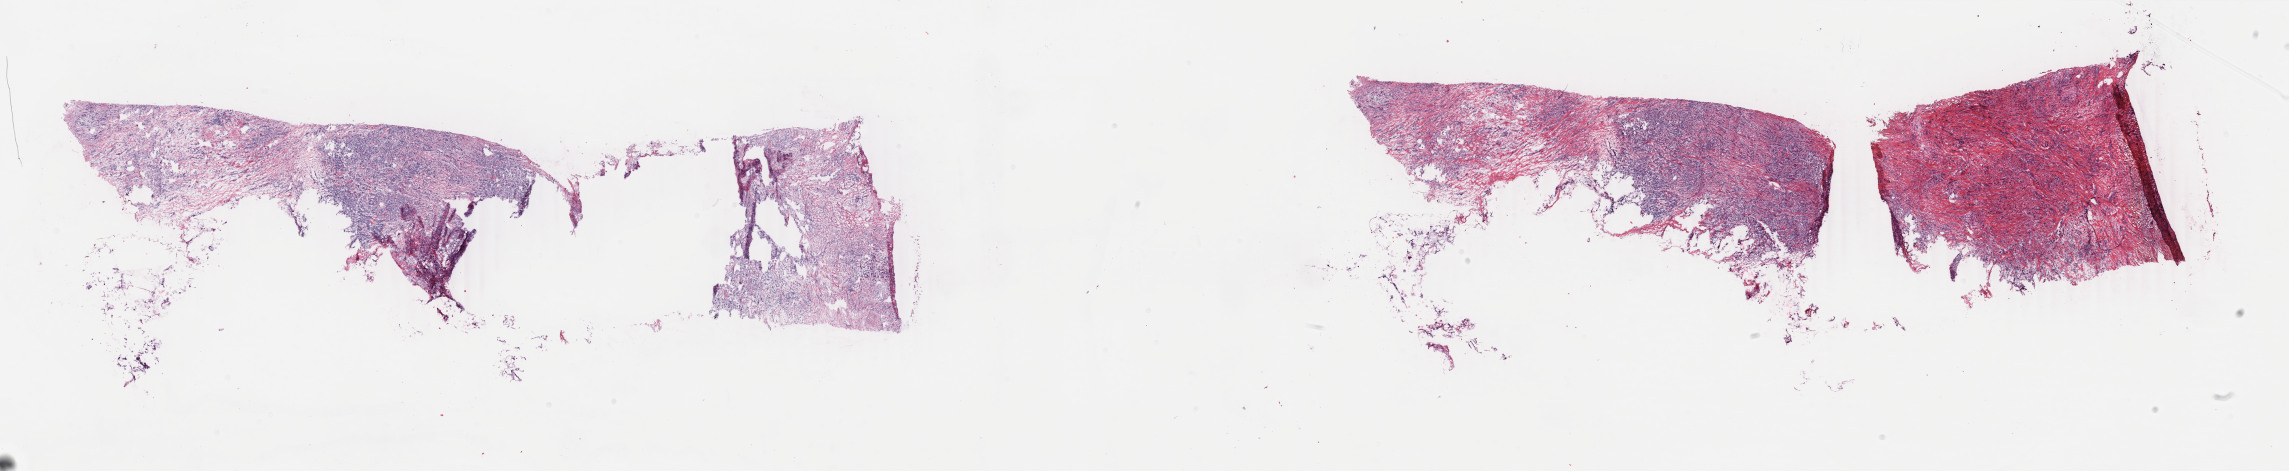
Digitized H&E tissue section (whole slide), whole scanned area (about 36.4 x 7.5 mm, slide scanned at 40x) shown as a low-resolution overview. Frozen section from the top of the tissue portion. Breast, primary tumour sample. Female patient; age at initial diagnosis 62 years. Pathologist review of this section (percent, as recorded): tumour cells 70%, tumour nuclei 80%.
Pathologic diagnosis: Lobular carcinoma, NOS.